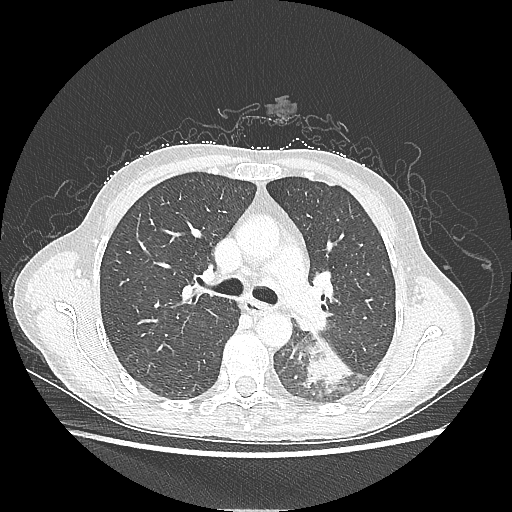
Chest CT, one axial slice; position 139 of 220 along the scan axis; 80 kVp; lung window (W 1500 / L -600 HU); 1.25 mm slice thickness; 512 × 512 image matrix. Patient: female, 53 years. From the clinical record (not read from this slice): clinical TNM (as recorded): T3 N0 M0.
Outlined on this slice (rectangle marked by the reading radiologist):
- lung tumour (recorded histology: adenocarcinoma): bounding box [x1, y1, x2, y2] px = [298, 337, 355, 390]